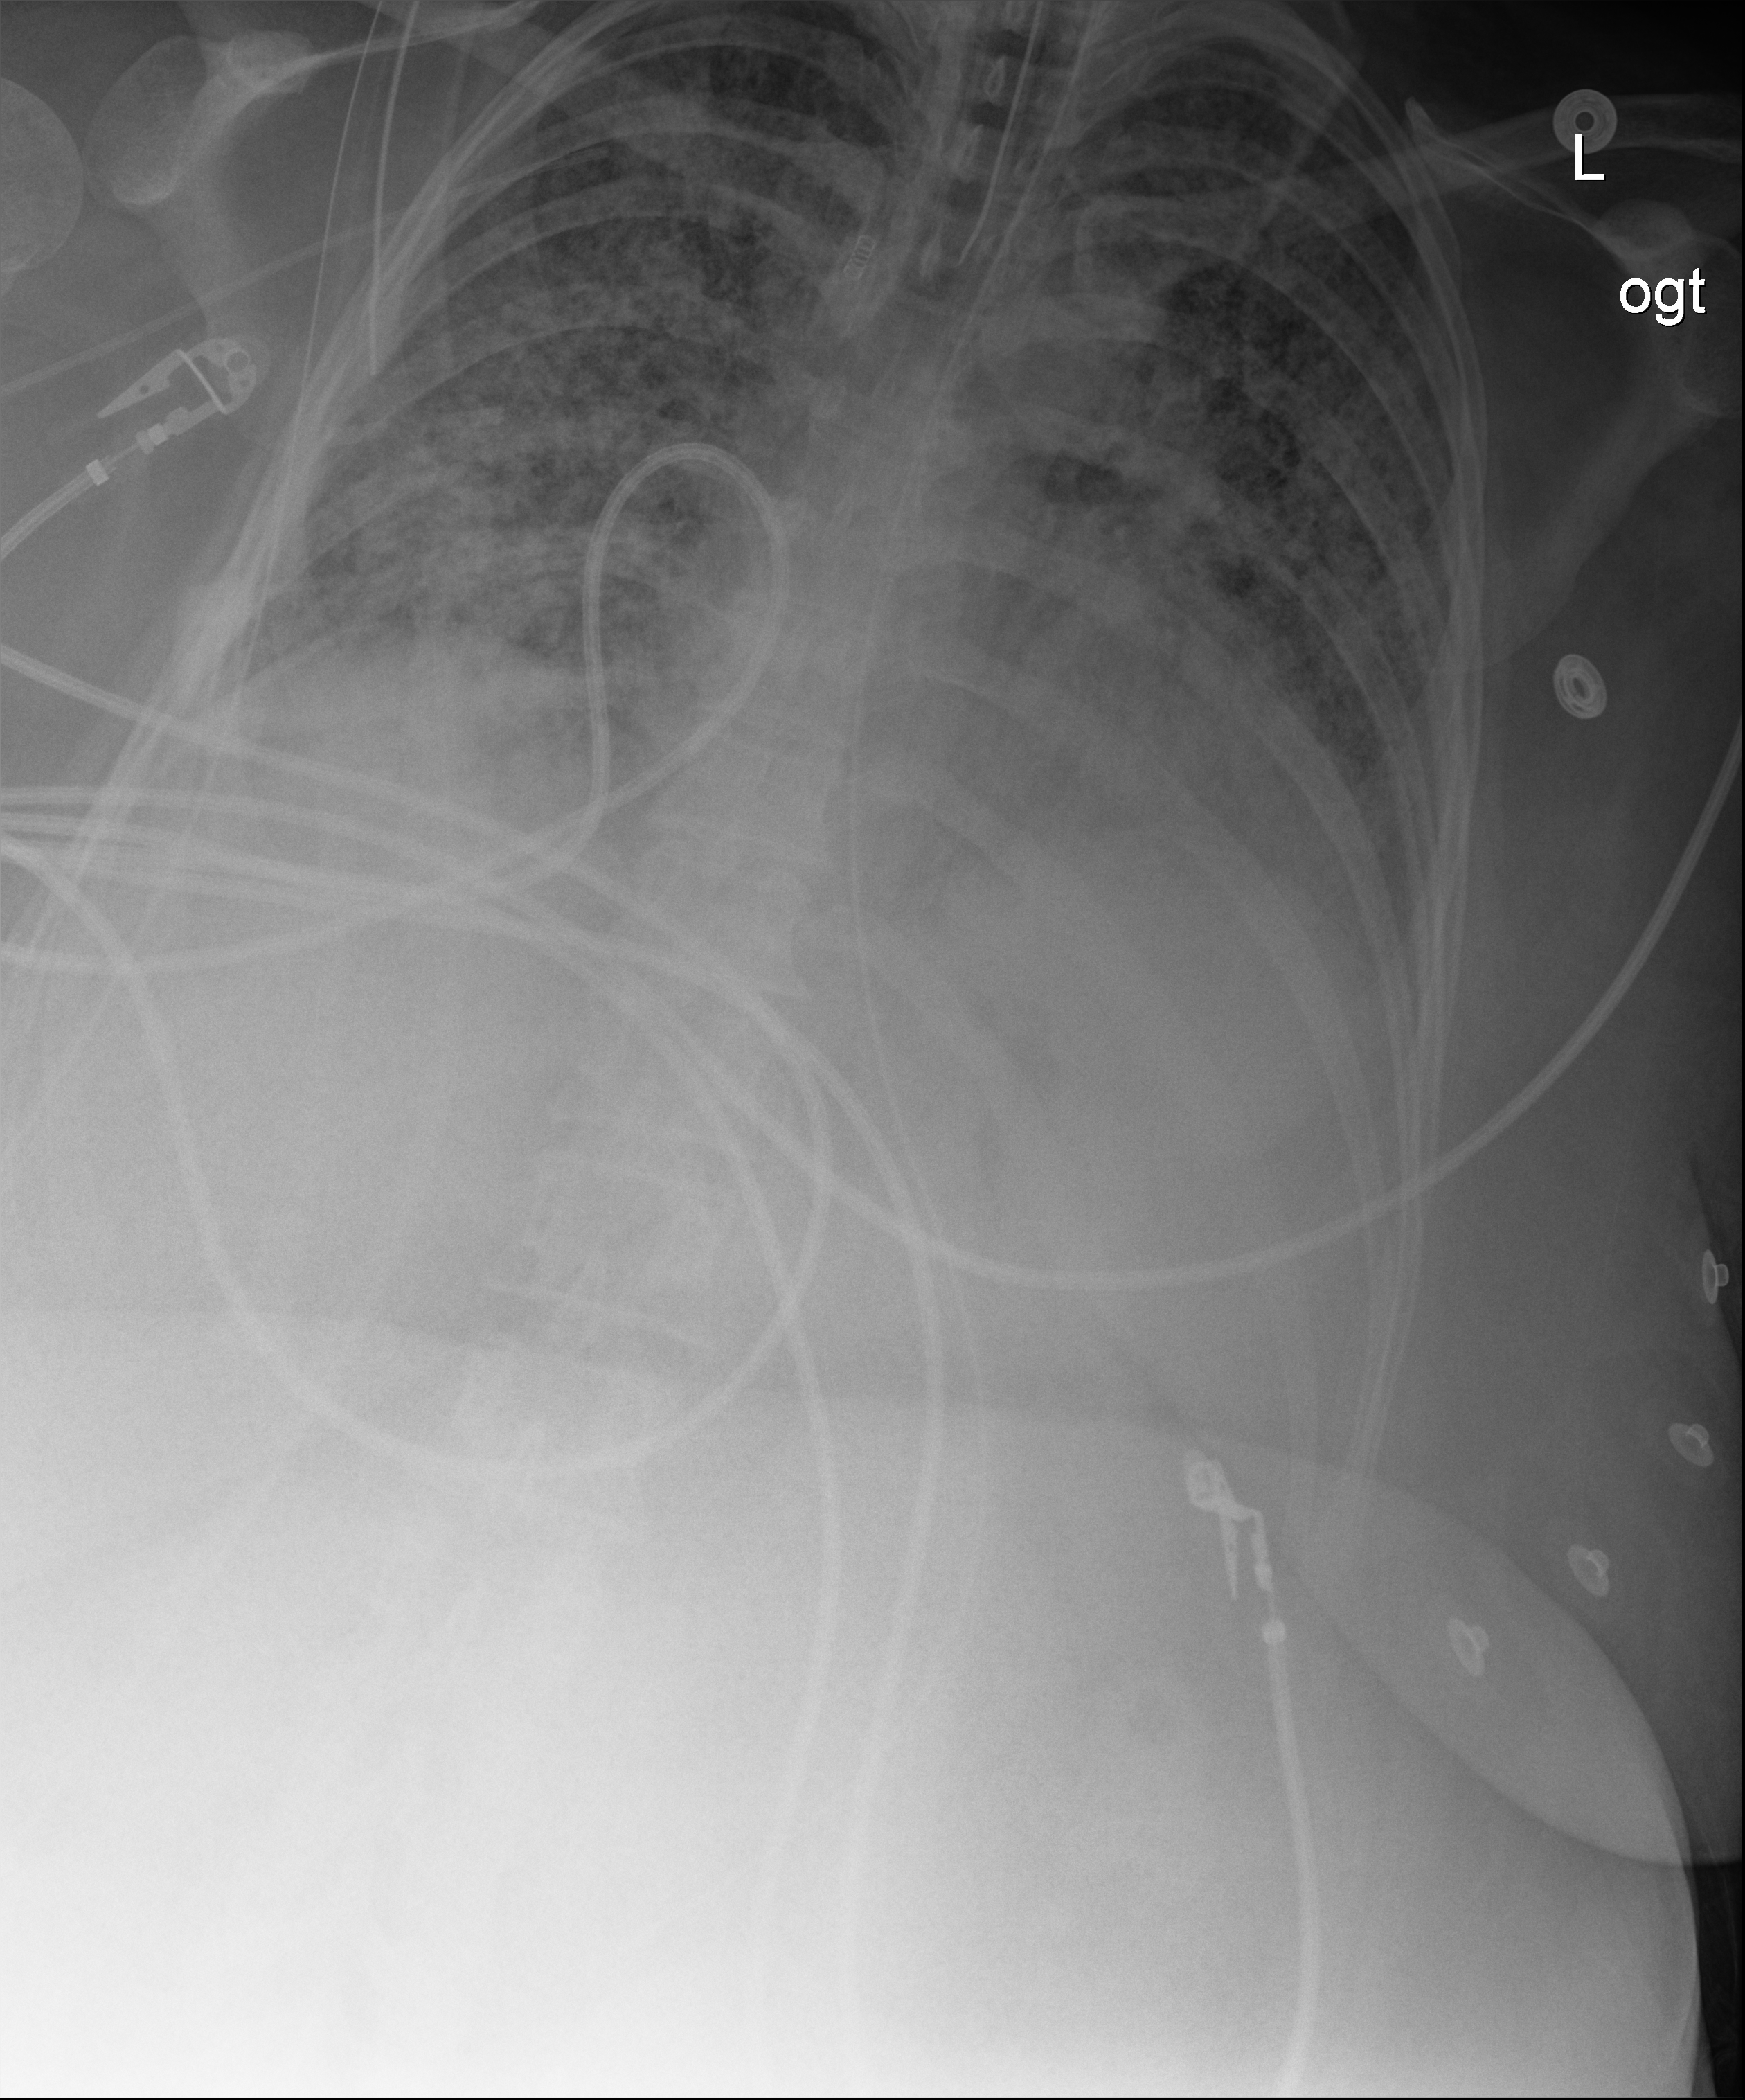
Portable chest radiograph. Female patient hospitalised with COVID-19, age 18–59 years.
Admission-level facts for this patient (not findings on this image; timing relative to this image not recorded): COPD (admission record): no.